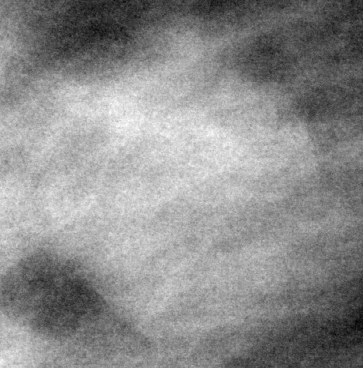
Cropped region of a digitized screen-film mammogram centred on a radiologist-marked abnormality; right breast; MLO view; BI-RADS breast density category 2 (scale 1–4).
- Finding: mass, shape lobulated, margins circumscribed; BI-RADS assessment category 3; pathology (as recorded): benign.